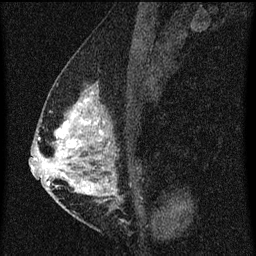
Breast MRI (dynamic contrast-enhanced), one sagittal slice; position 29 of 60 along the scan axis; dynamic contrast-enhanced series, image 2 of 3 at this slice position (ordered by acquisition); 1.5 T; TE 4.2 ms, TR 8 ms; 2 mm slice thickness; 256 × 256 image matrix, field of view 180 × 180 mm. Female patient, age 47 years.
Structures marked on this image (semi-automatically segmented with operator editing):
- analysis volume of interest (the breast-tissue region the enhancement analysis was run in; not a lesion): box from (x=50, y=80) to (x=138, y=203) px
- tumour enhancement mask (voxels above the 70 % enhancement threshold inside the analysis volume of interest): (x=50, y=92)–(x=115, y=195)